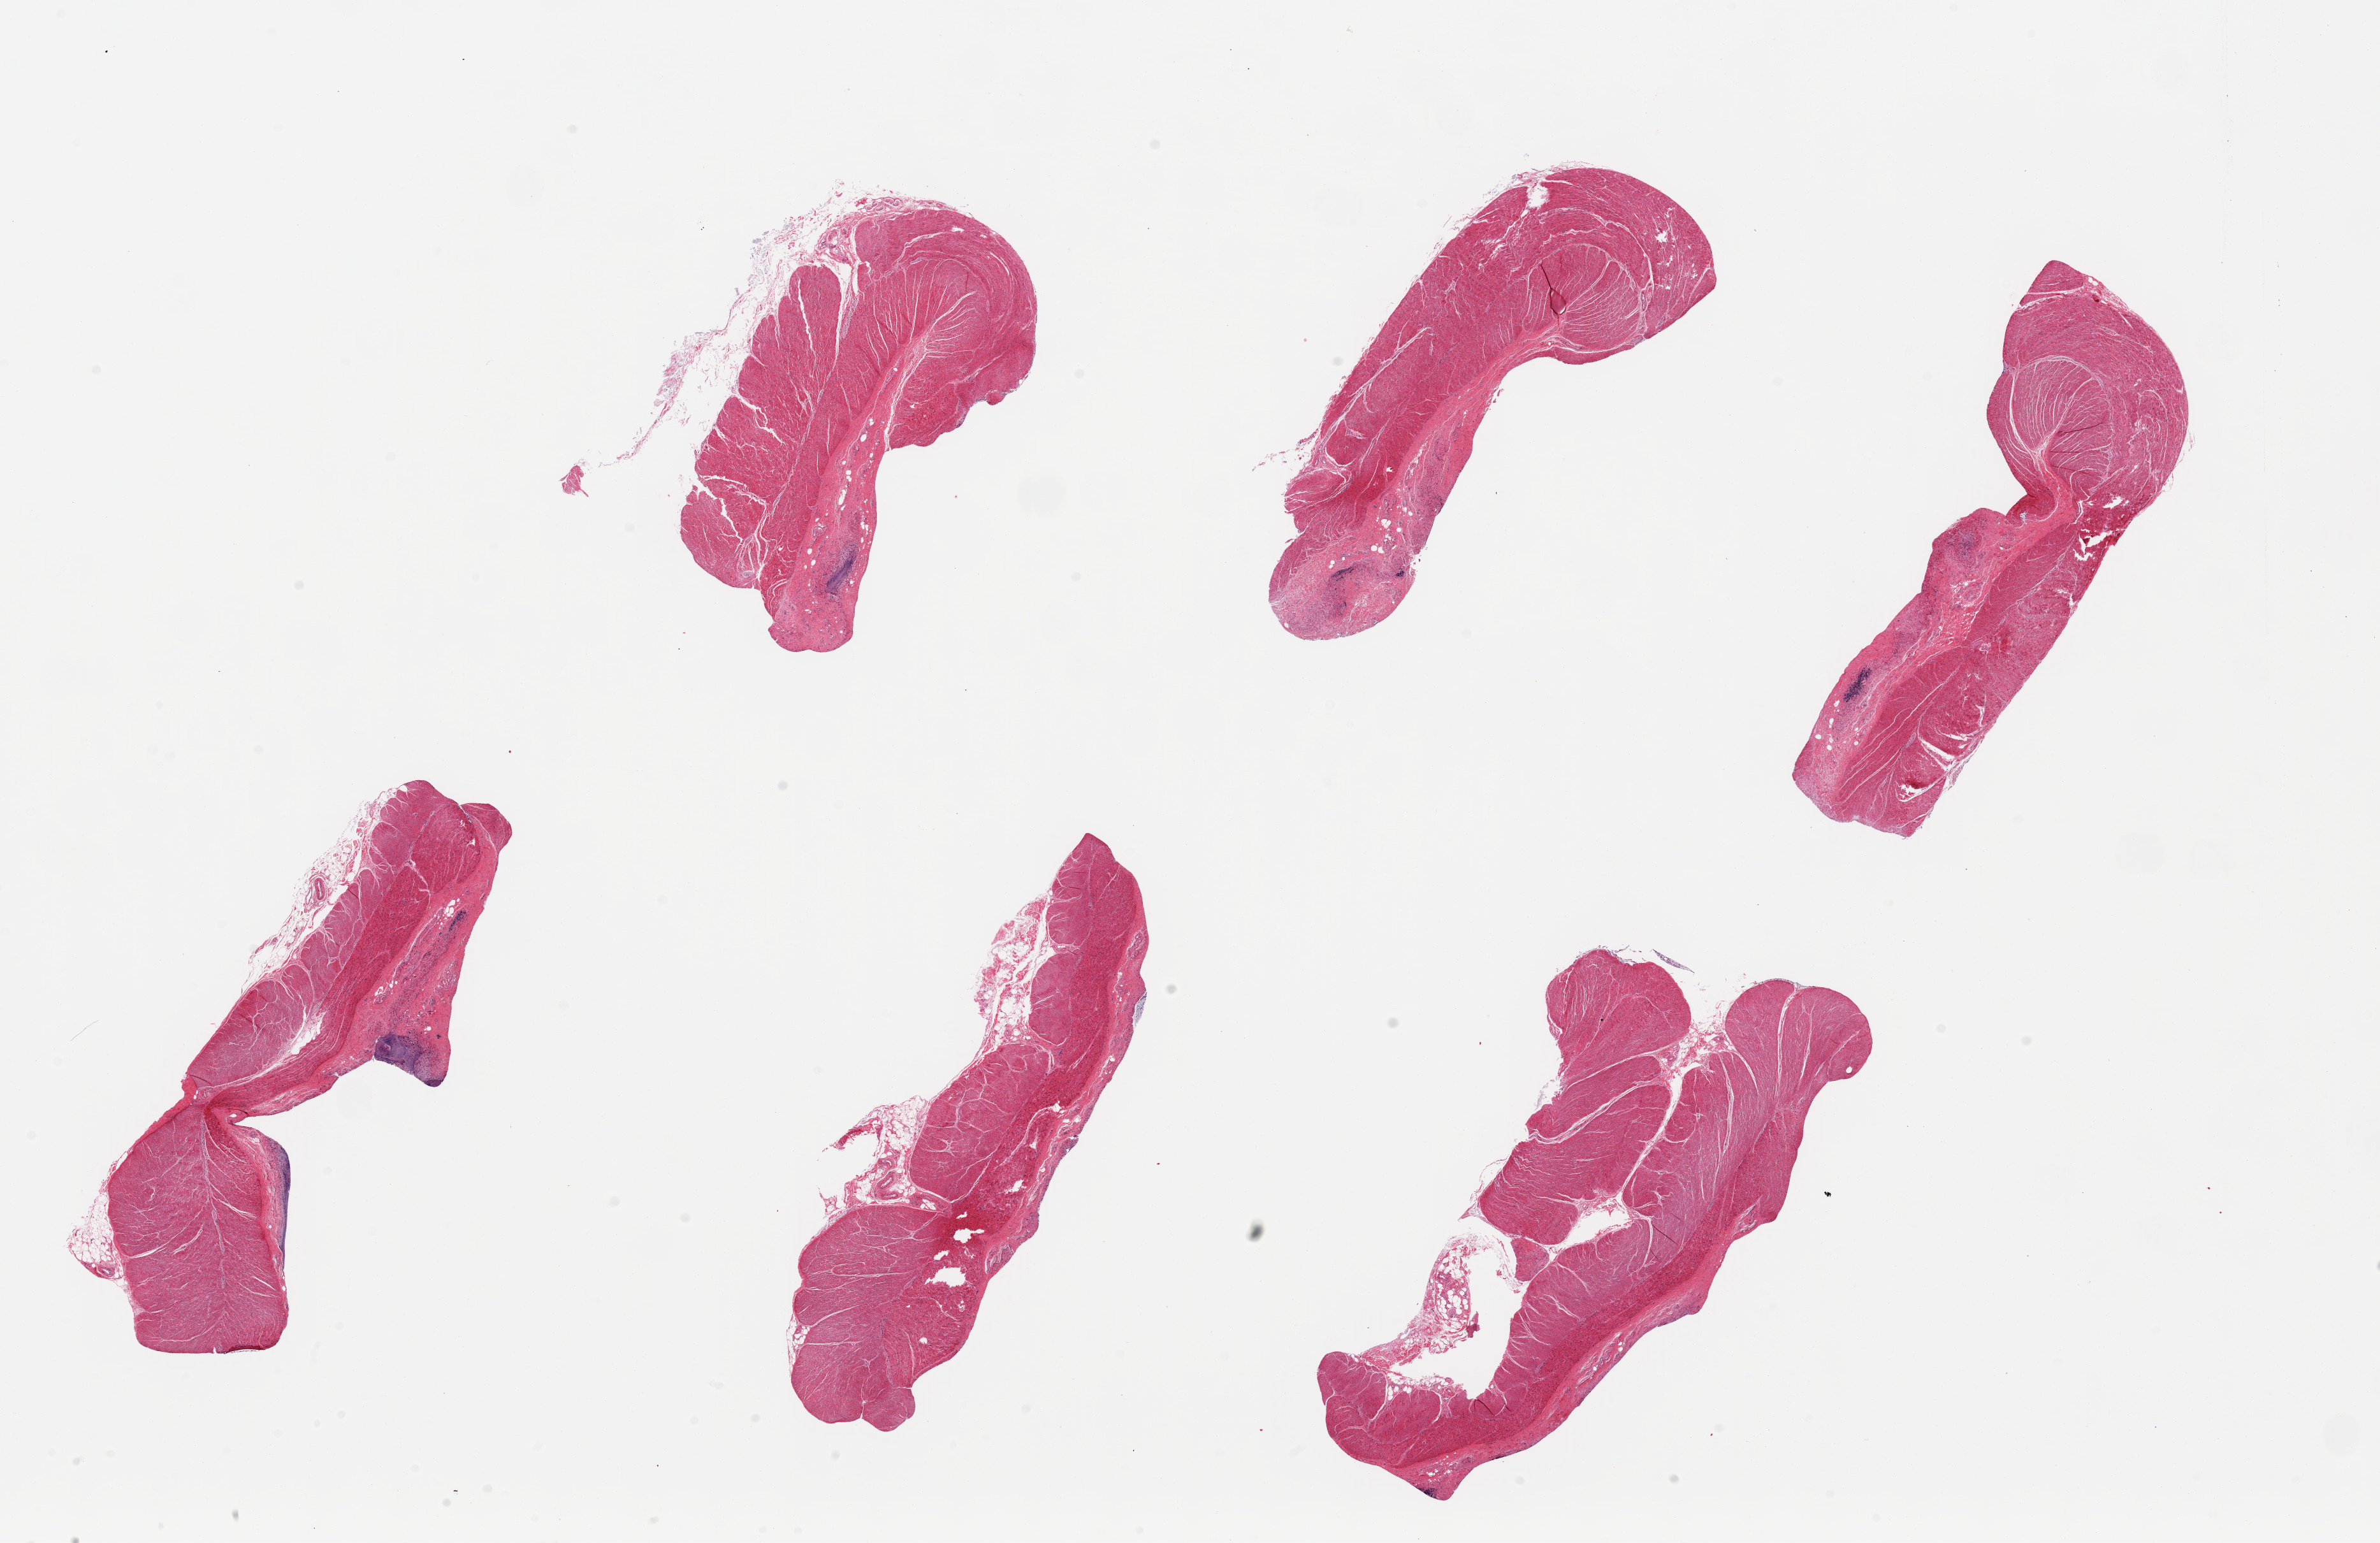
Digitized H&E-stained section — shown as a low-resolution overview of the whole scanned area (about 29.5 x 19.1 mm), PAXgene-fixed paraffin-embedded (PFPE) section, target tissue: sigmoid colon, tissue donor sample. Donor sex: female.
Review note (as recorded): 6 pieces. up to 8x4mm; muscularis and submucosal stroma.